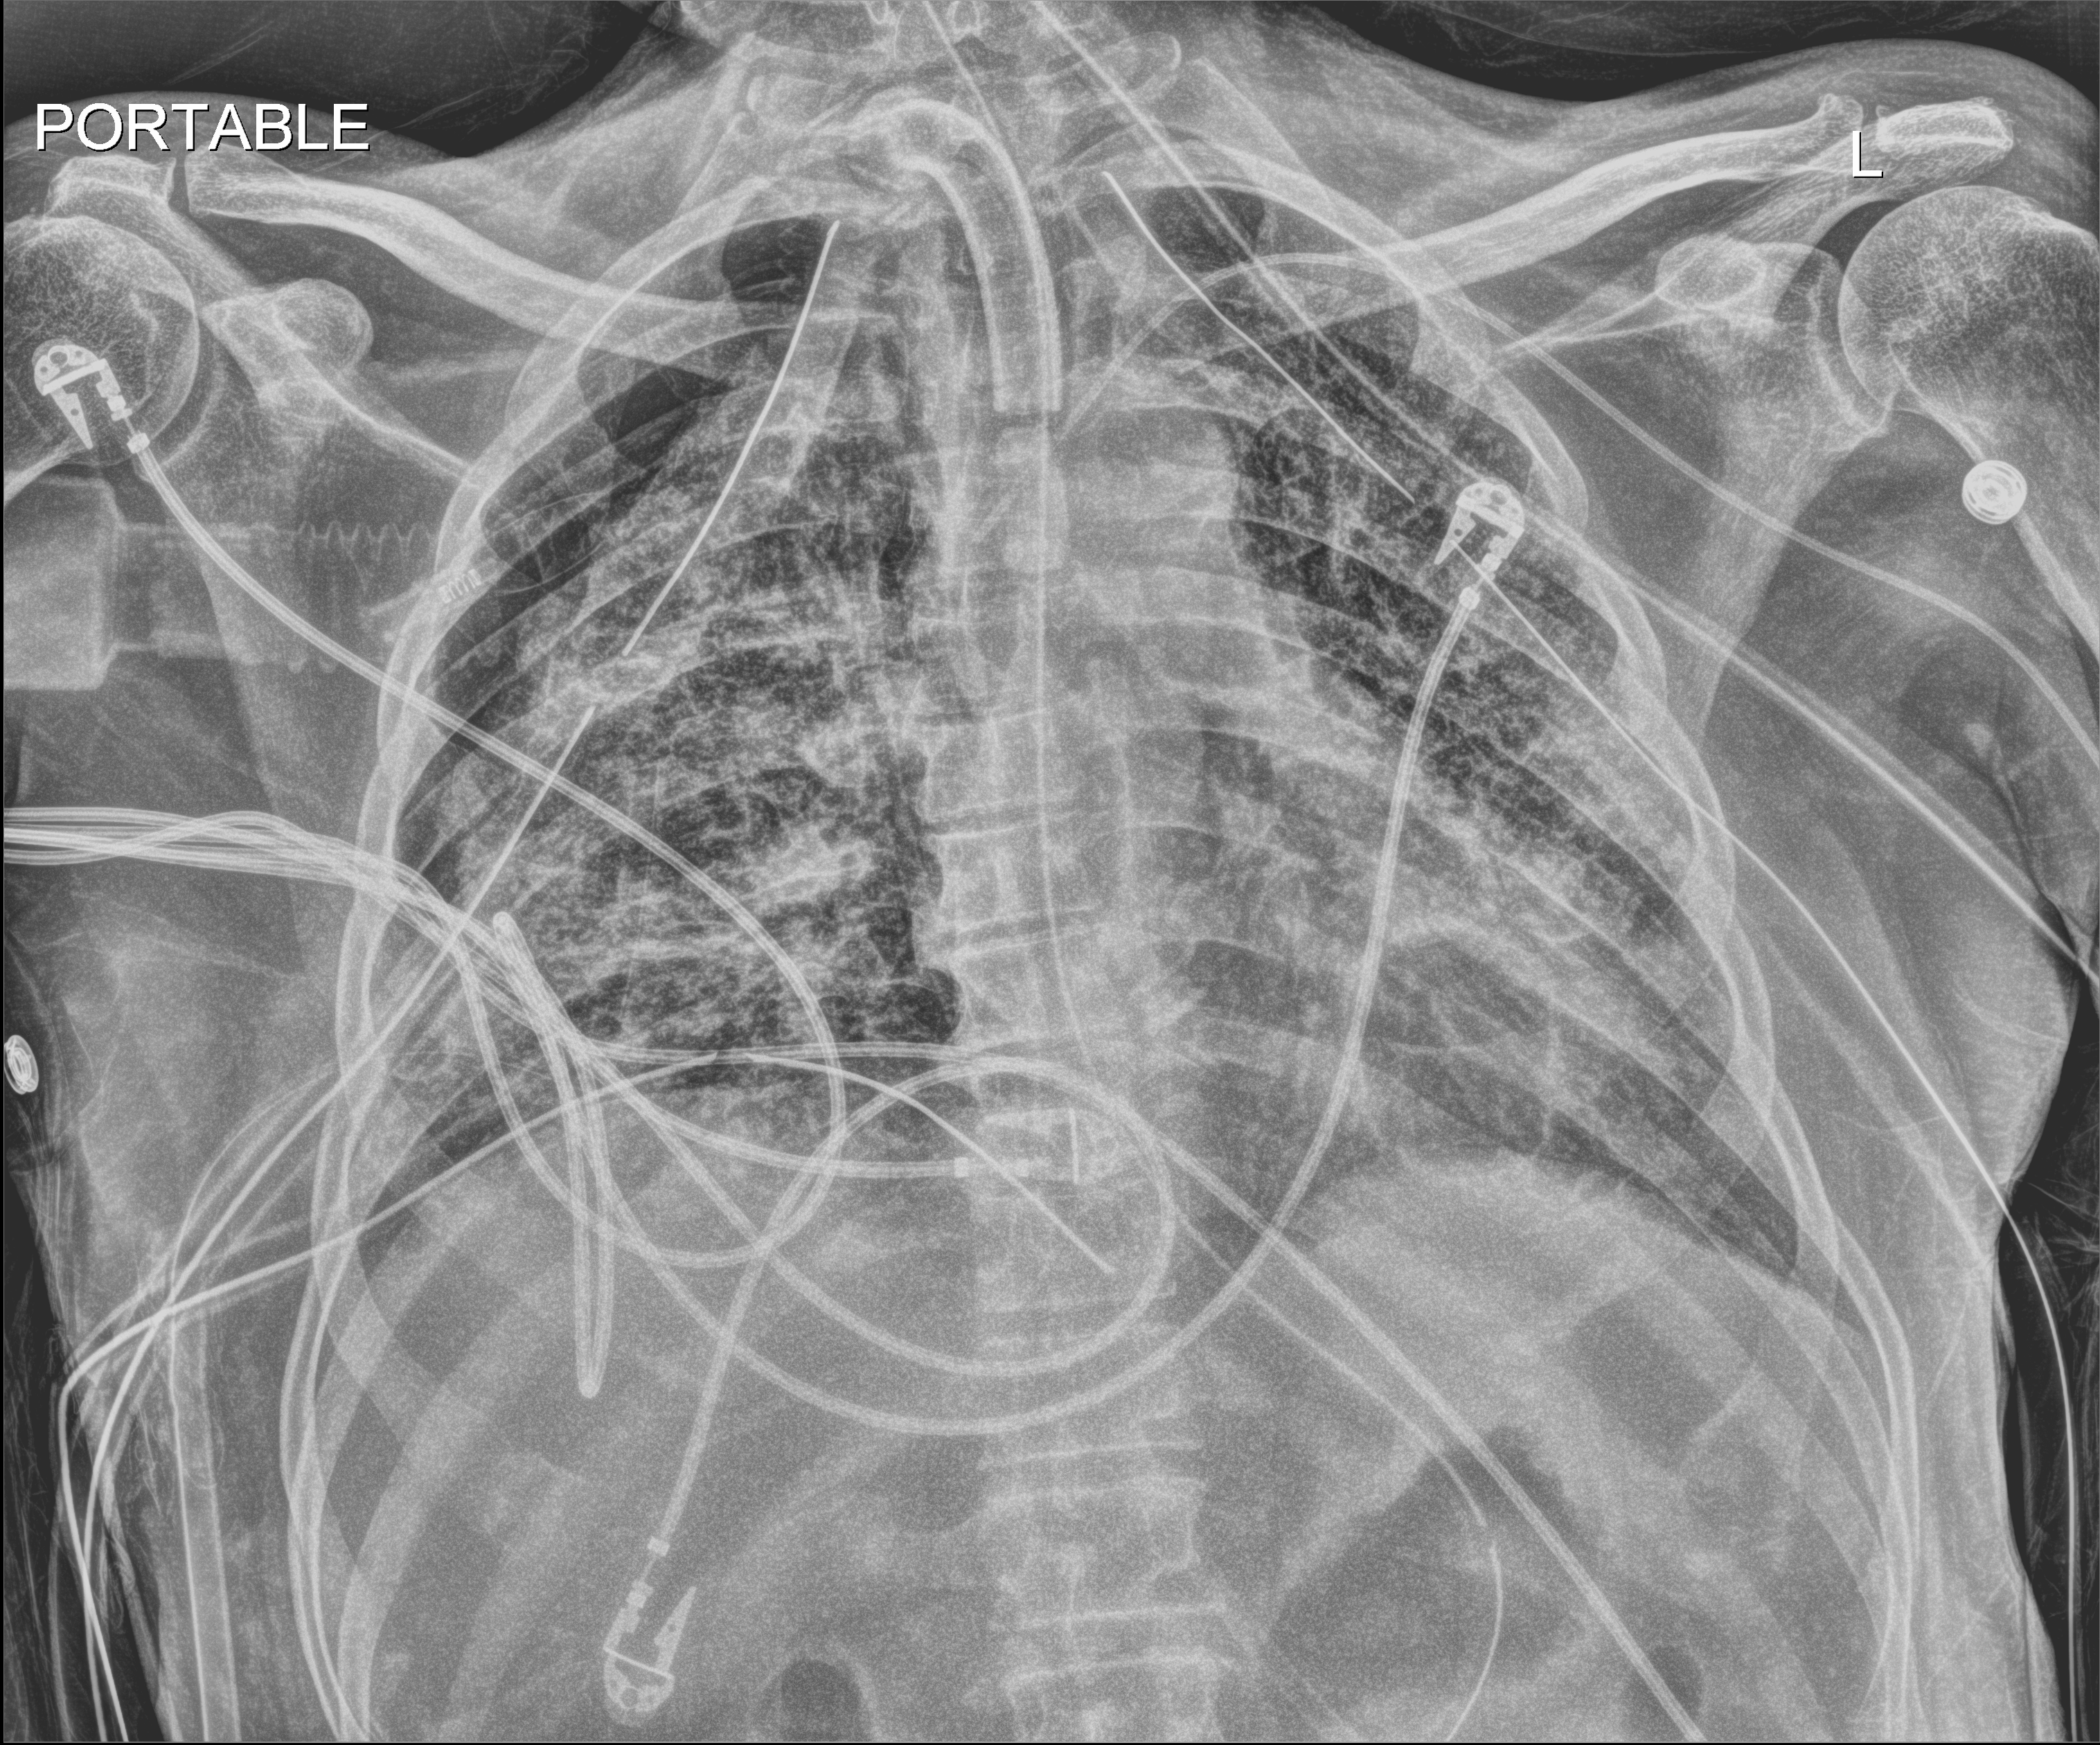
Bedside chest radiograph (digital radiography). Patient hospitalised with COVID-19; male, aged 18–59 years.
Admission-level facts for this patient (not findings on this image; timing relative to this image not recorded): mechanically ventilated during this hospital stay: yes; admitted to intensive care during this hospital stay: yes.